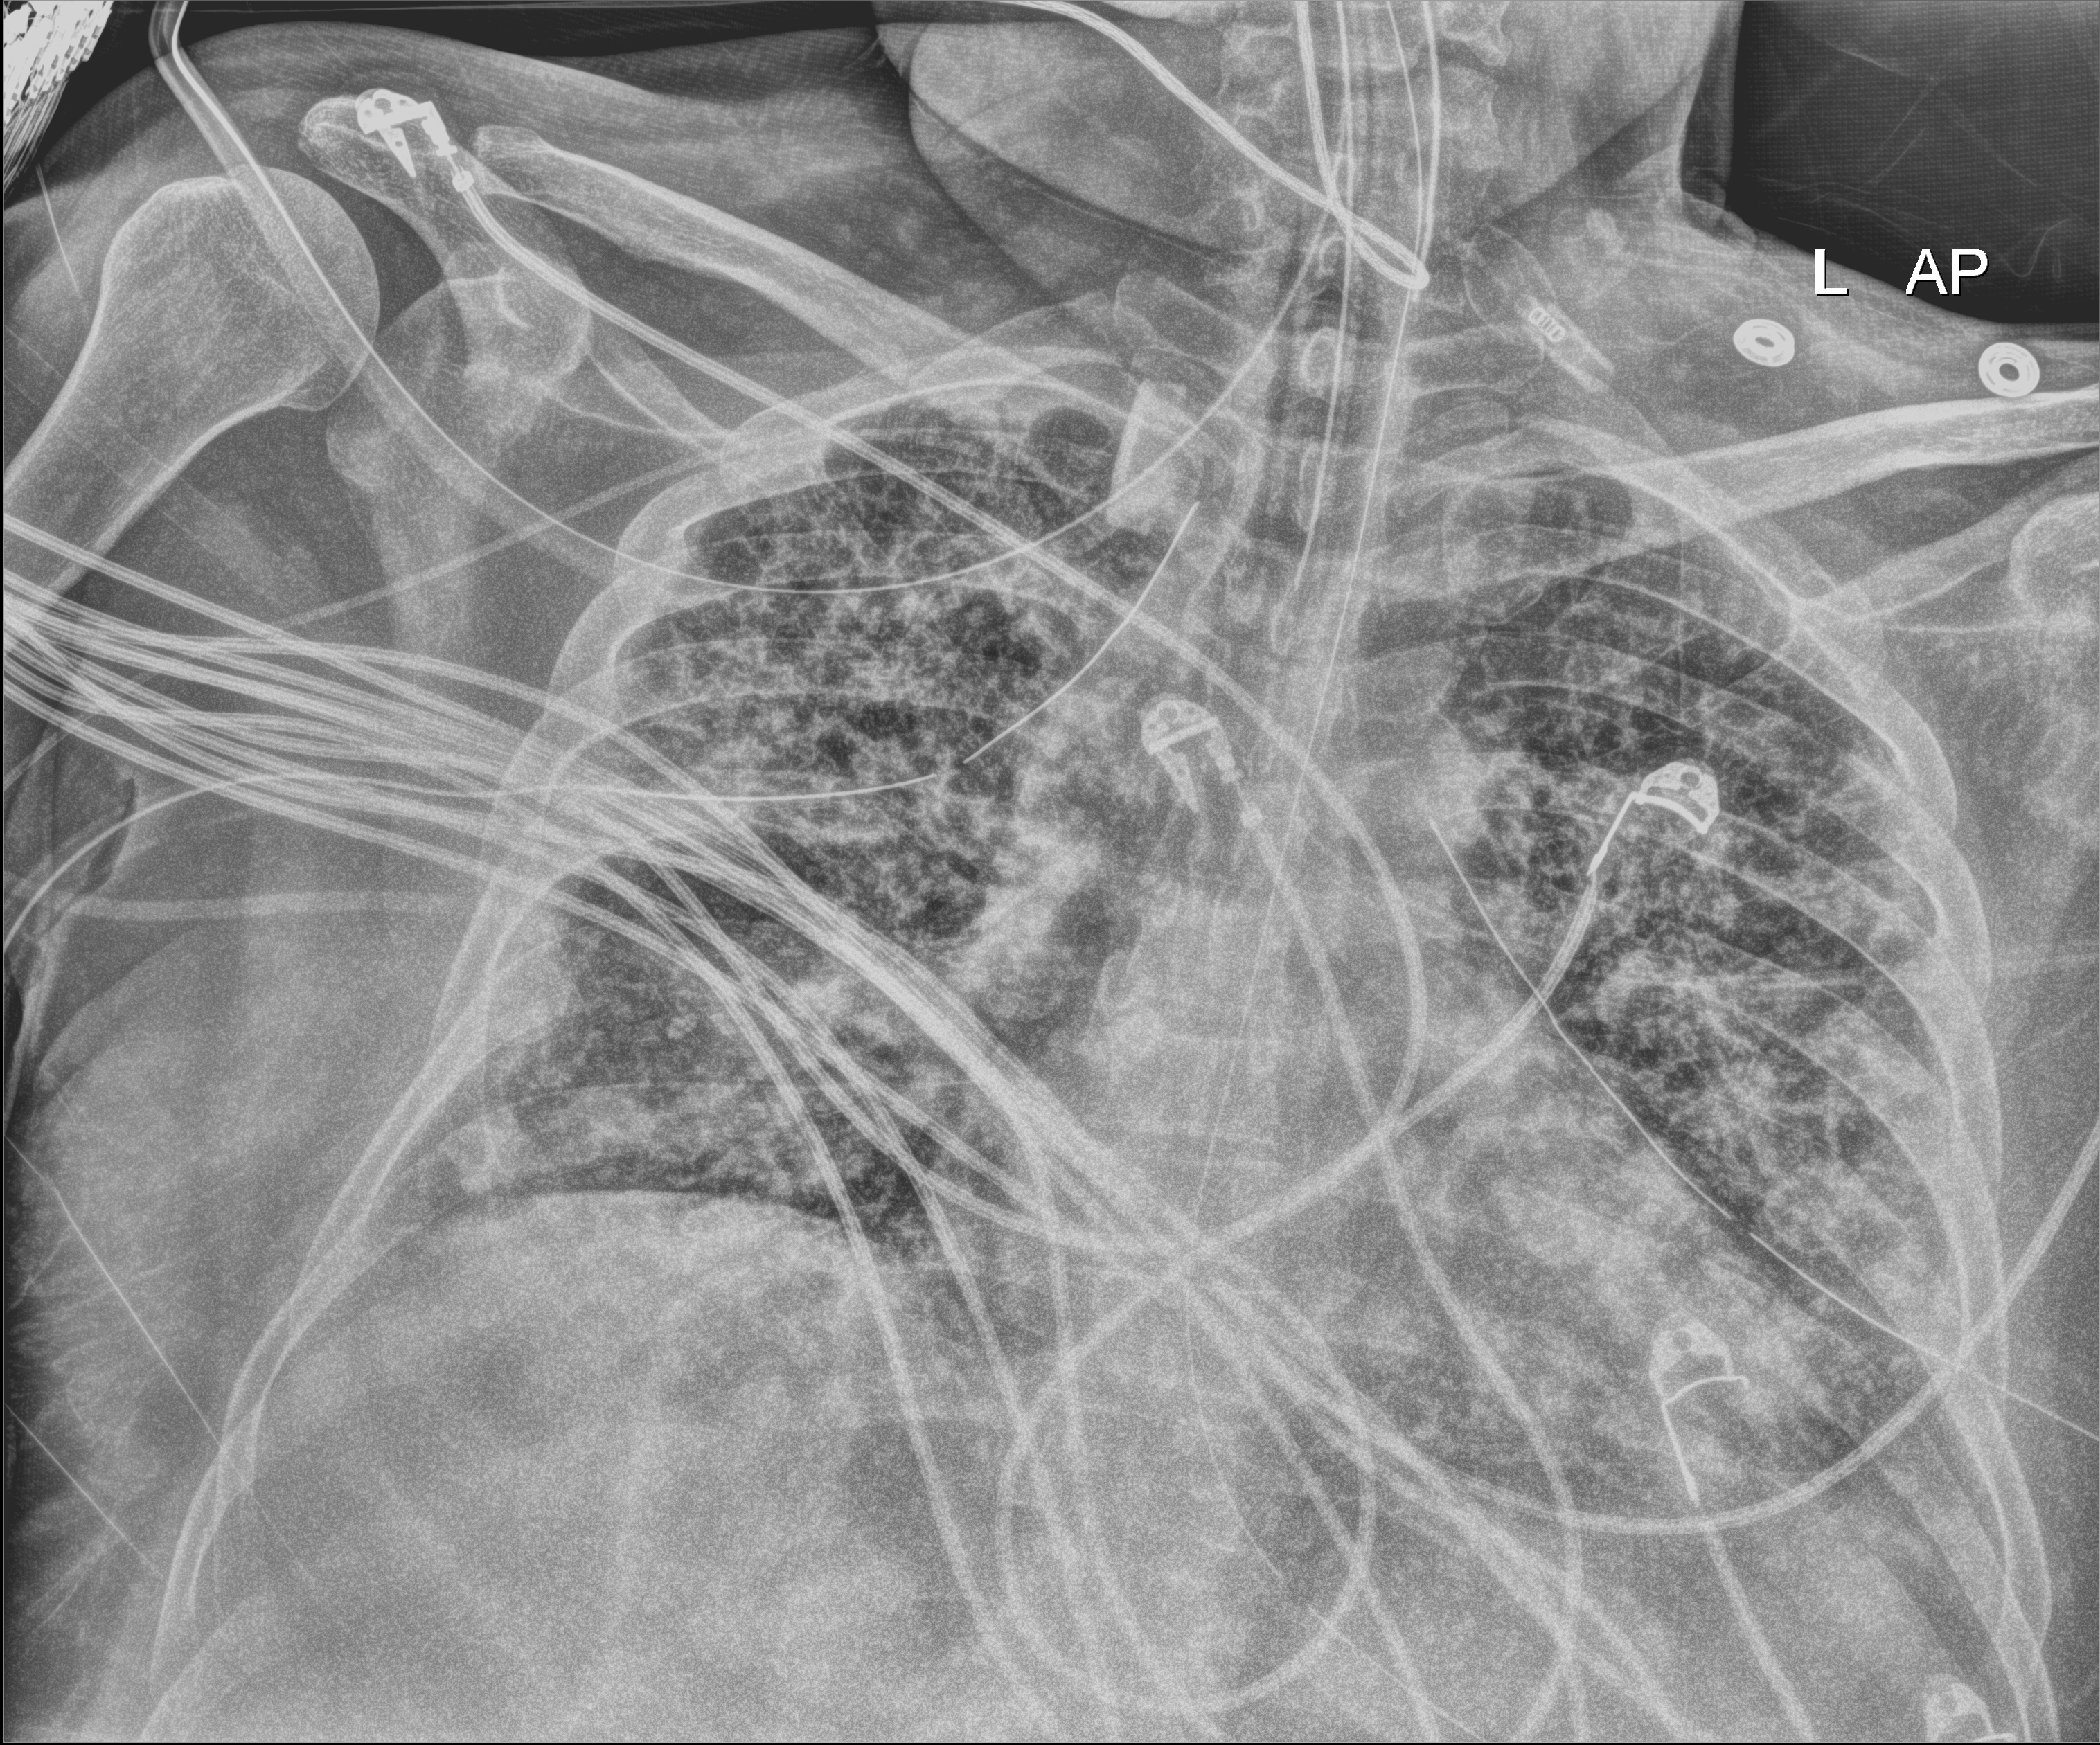
Bedside chest radiograph (digital radiography), anteroposterior (AP) projection. Patient hospitalised with COVID-19; male, aged 18–59 years.
Admission-level facts for this patient (not findings on this image; timing relative to this image not recorded): admitted to intensive care during this hospital stay: yes; chronic kidney disease (admission record): no; mechanically ventilated during this hospital stay: yes.